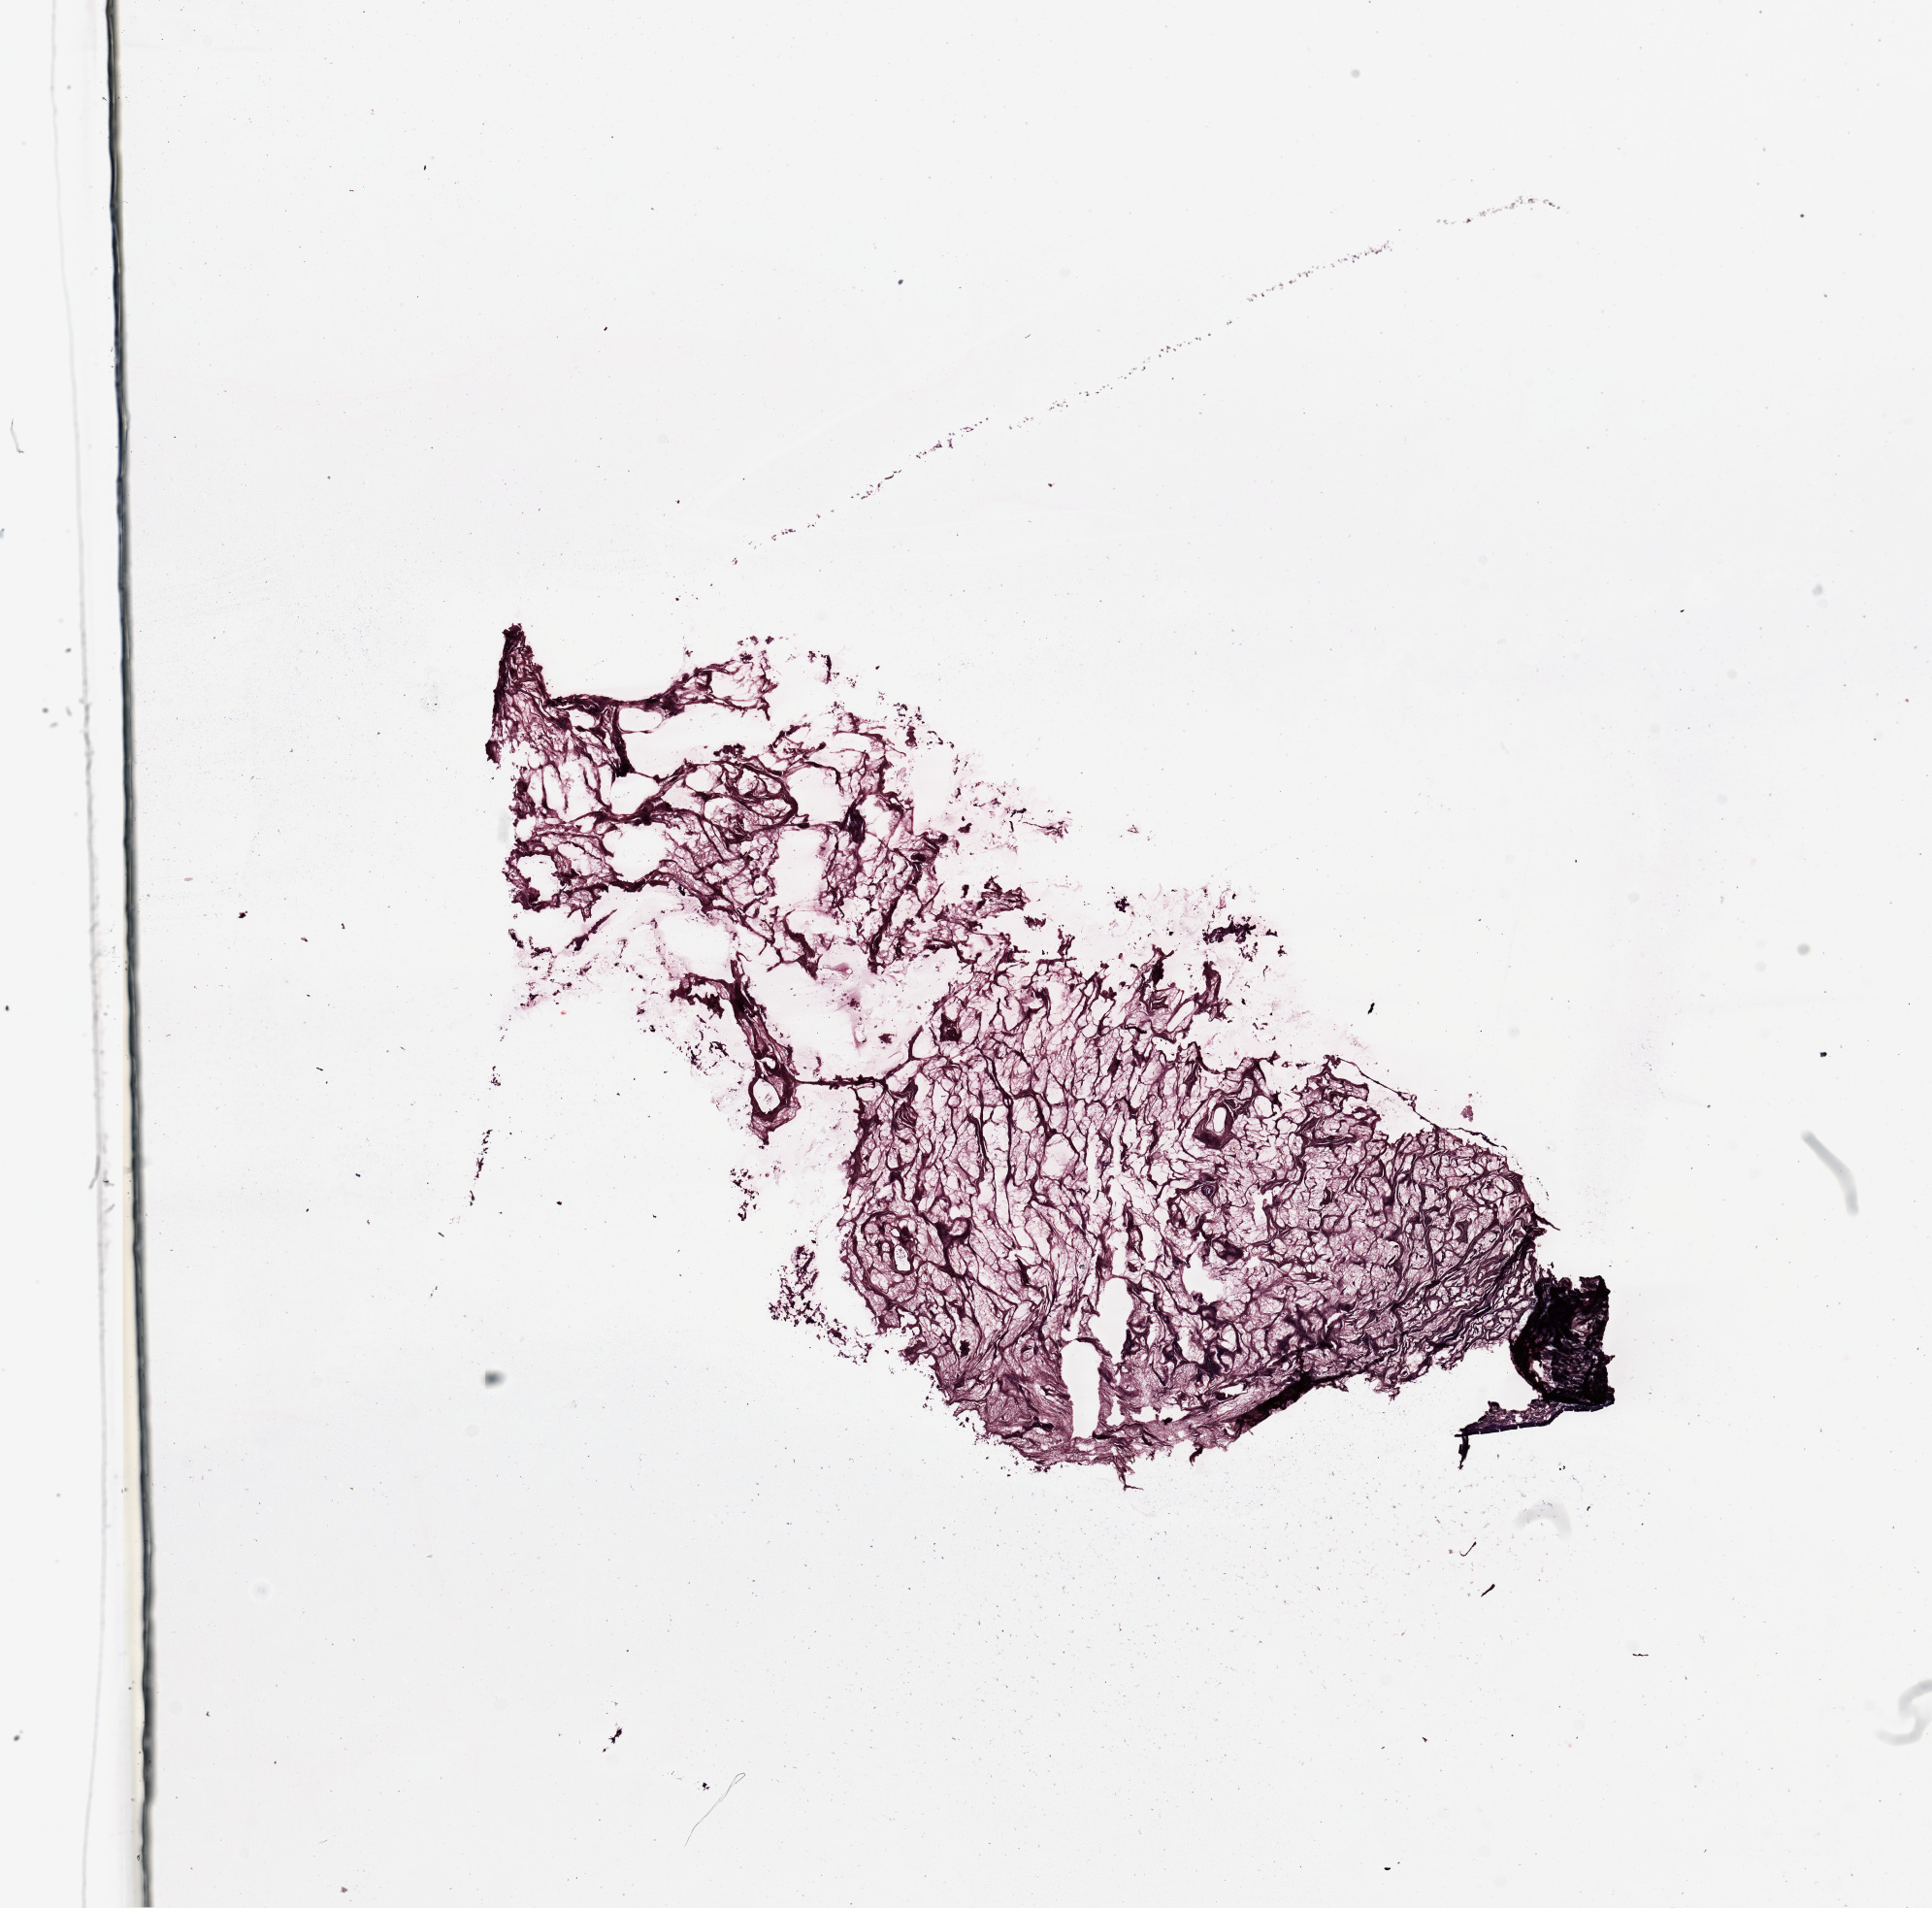
Digitized H&E-stained tissue section (whole slide) — low-resolution overview of the scanned area, about 15.8 x 15.6 mm; uterus, normal (non-tumour) tissue. Female, 78 y/o.
This section: normal (non-tumour) tissue from the same patient. Patient diagnosis: Endometrioid adenocarcinoma, NOS.